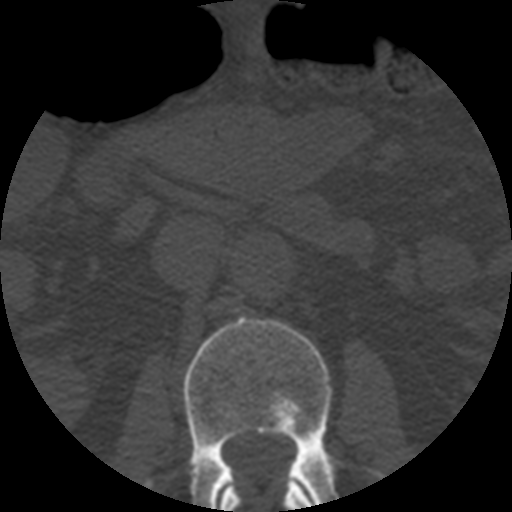
CT including the spine, one axial slice. Position 160 of 508 along the scan axis. 120 kVp. Bone window (W 1800 / L 400 HU). 1.25 mm slice thickness. 512 × 512 image matrix, field of view 160 × 160 mm. Patient age 57 years. Case-level facts recorded for this patient, not image findings: primary cancer: prostate.
Outlined on this slice (semi-automatic segmentation, software-assisted and operator-edited):
- L1 vertebra: box from (x=220, y=482) to (x=314, y=512) px
- L2 vertebra: (x=147, y=318)–(x=384, y=512)